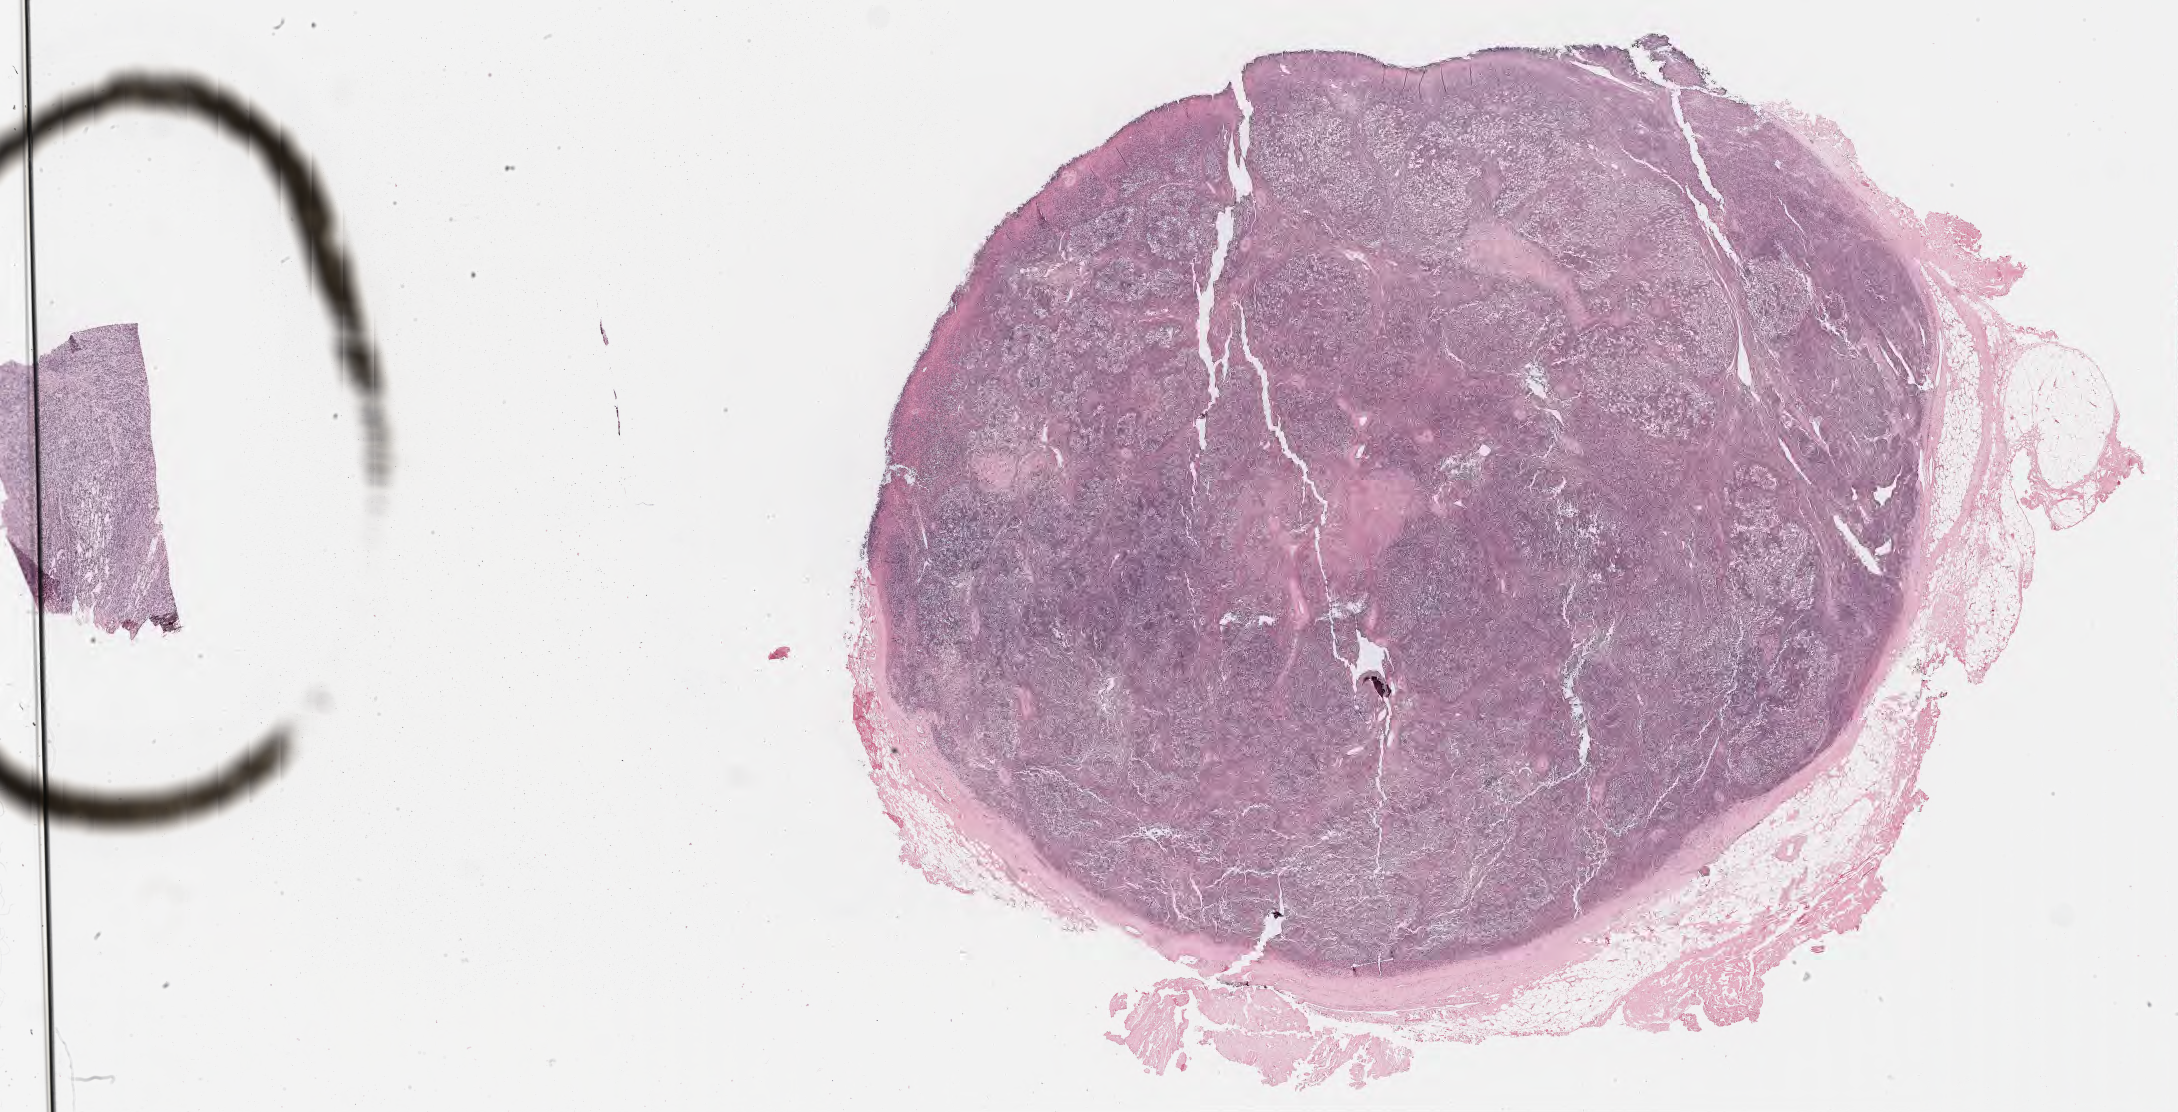
Whole-slide image; stain recorded as Iodonitrotetrazolium — low-resolution overview of the scanned area, about 35.2 x 18.0 mm, specimen: tumor tissue, site: lymph node. Patient: male, aged 46.
Histologic diagnosis: Diffuse large B-cell lymphoma, NOS.